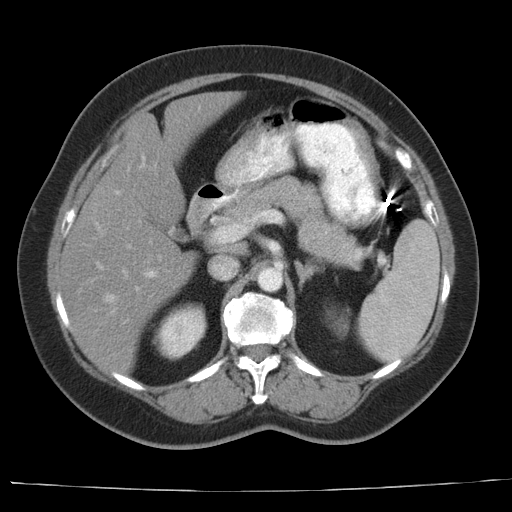
Contrast-enhanced abdominal CT, one axial slice. Slice 18 of 44 in the series (ordered by position). Reconstruction kernel AA-1. 140 kVp. Intravenous contrast given. Soft-tissue window (W 400 / L 40 HU). 512 × 512 image matrix. Female patient. From the clinical record (not read from this slice): diagnosis: colorectal cancer liver metastases, imaged before liver resection; multiple liver metastases: yes; largest metastasis: 1.8 cm; disease in both lobes: no.
Annotated regions visible in this slice (expert manual segmentation):
- hepatic veins: bounding box (x1, y1, x2, y2) in pixels: (106, 191, 119, 312)
- liver: (60, 92, 240, 374)
- planned liver remnant (the part of the liver to remain after resection): (108, 93, 241, 223)
- portal vein (with intrahepatic branches): (97, 156, 155, 322)